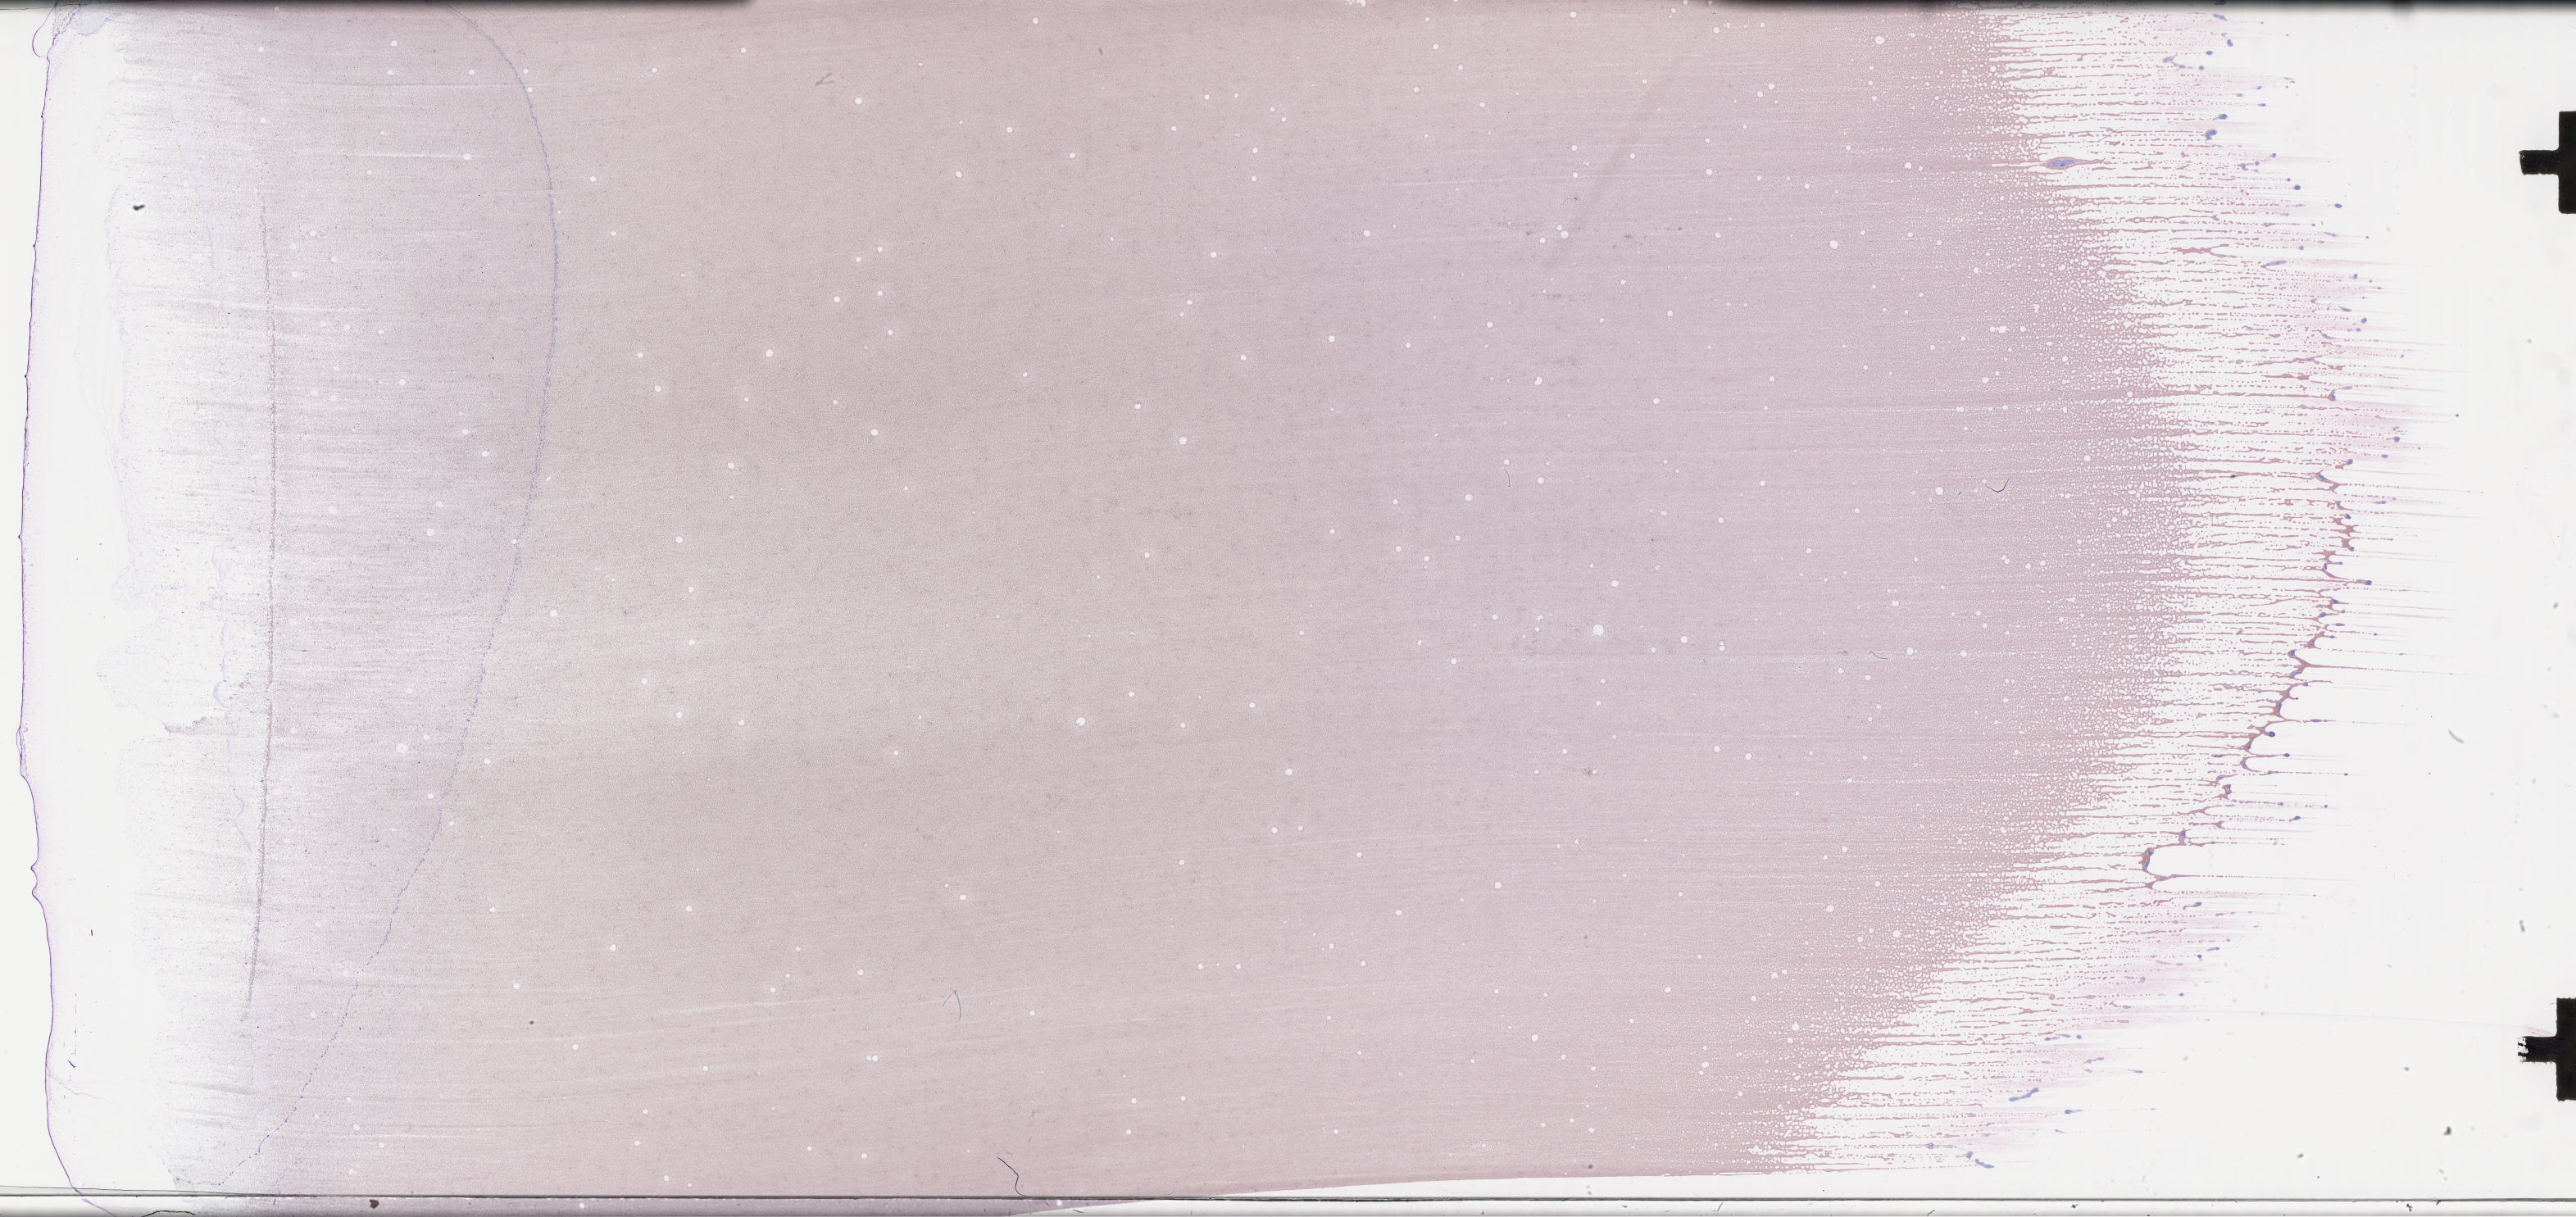
Wright-Giemsa-stained whole blood smear, whole-slide image, a low-resolution overview of the entire scanned area, about 50.8 x 24.0 mm; EDTA-anticoagulated smear; collected on treatment. Patient sex: male.
Patient diagnosis: Plasma Cell Myeloma.